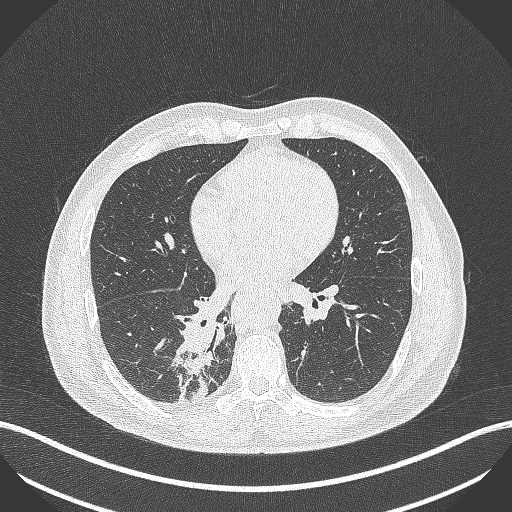
Chest CT, one axial slice; slice 214 of 451 in the series (ordered by position); lung window (W 1500 / L -600 HU); 1 mm slice thickness; 512 × 512 image matrix, field of view 400 × 400 mm. Male patient, age 61 years. Case-level facts recorded for this patient, not image findings: clinical TNM (as recorded): T1 N0 M0.
Outlined on this slice (bounding box drawn by a radiologist):
- lung tumour (recorded histology: small cell carcinoma): bounding box [x1, y1, x2, y2] px = [176, 311, 215, 399]